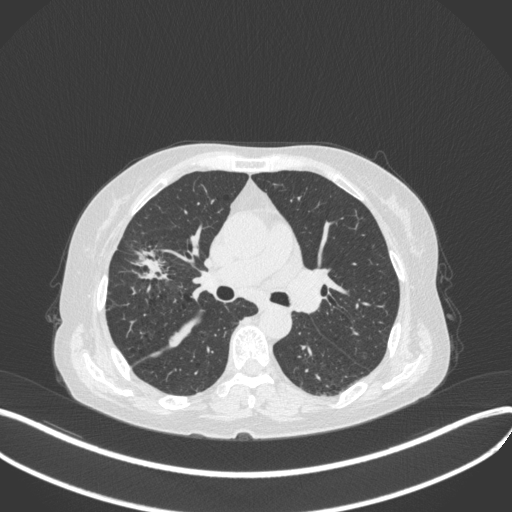
Chest CT, one axial slice. Slice 239 of 429 in the series (ordered by position). Reconstruction kernel B31f. Lung window (W 1500 / L -600 HU). 1 mm slice thickness. 512 × 512 image matrix, field of view 400 × 400 mm. Patient: female, 69 years. From the clinical record (not read from this slice): clinical TNM (as recorded): T1b N3 M0.
Annotated regions visible in this slice (bounding box drawn by a radiologist):
- lung tumour (recorded histology: small cell carcinoma): bounding box <120,243,175,287> (left, top, right, bottom; pixels)